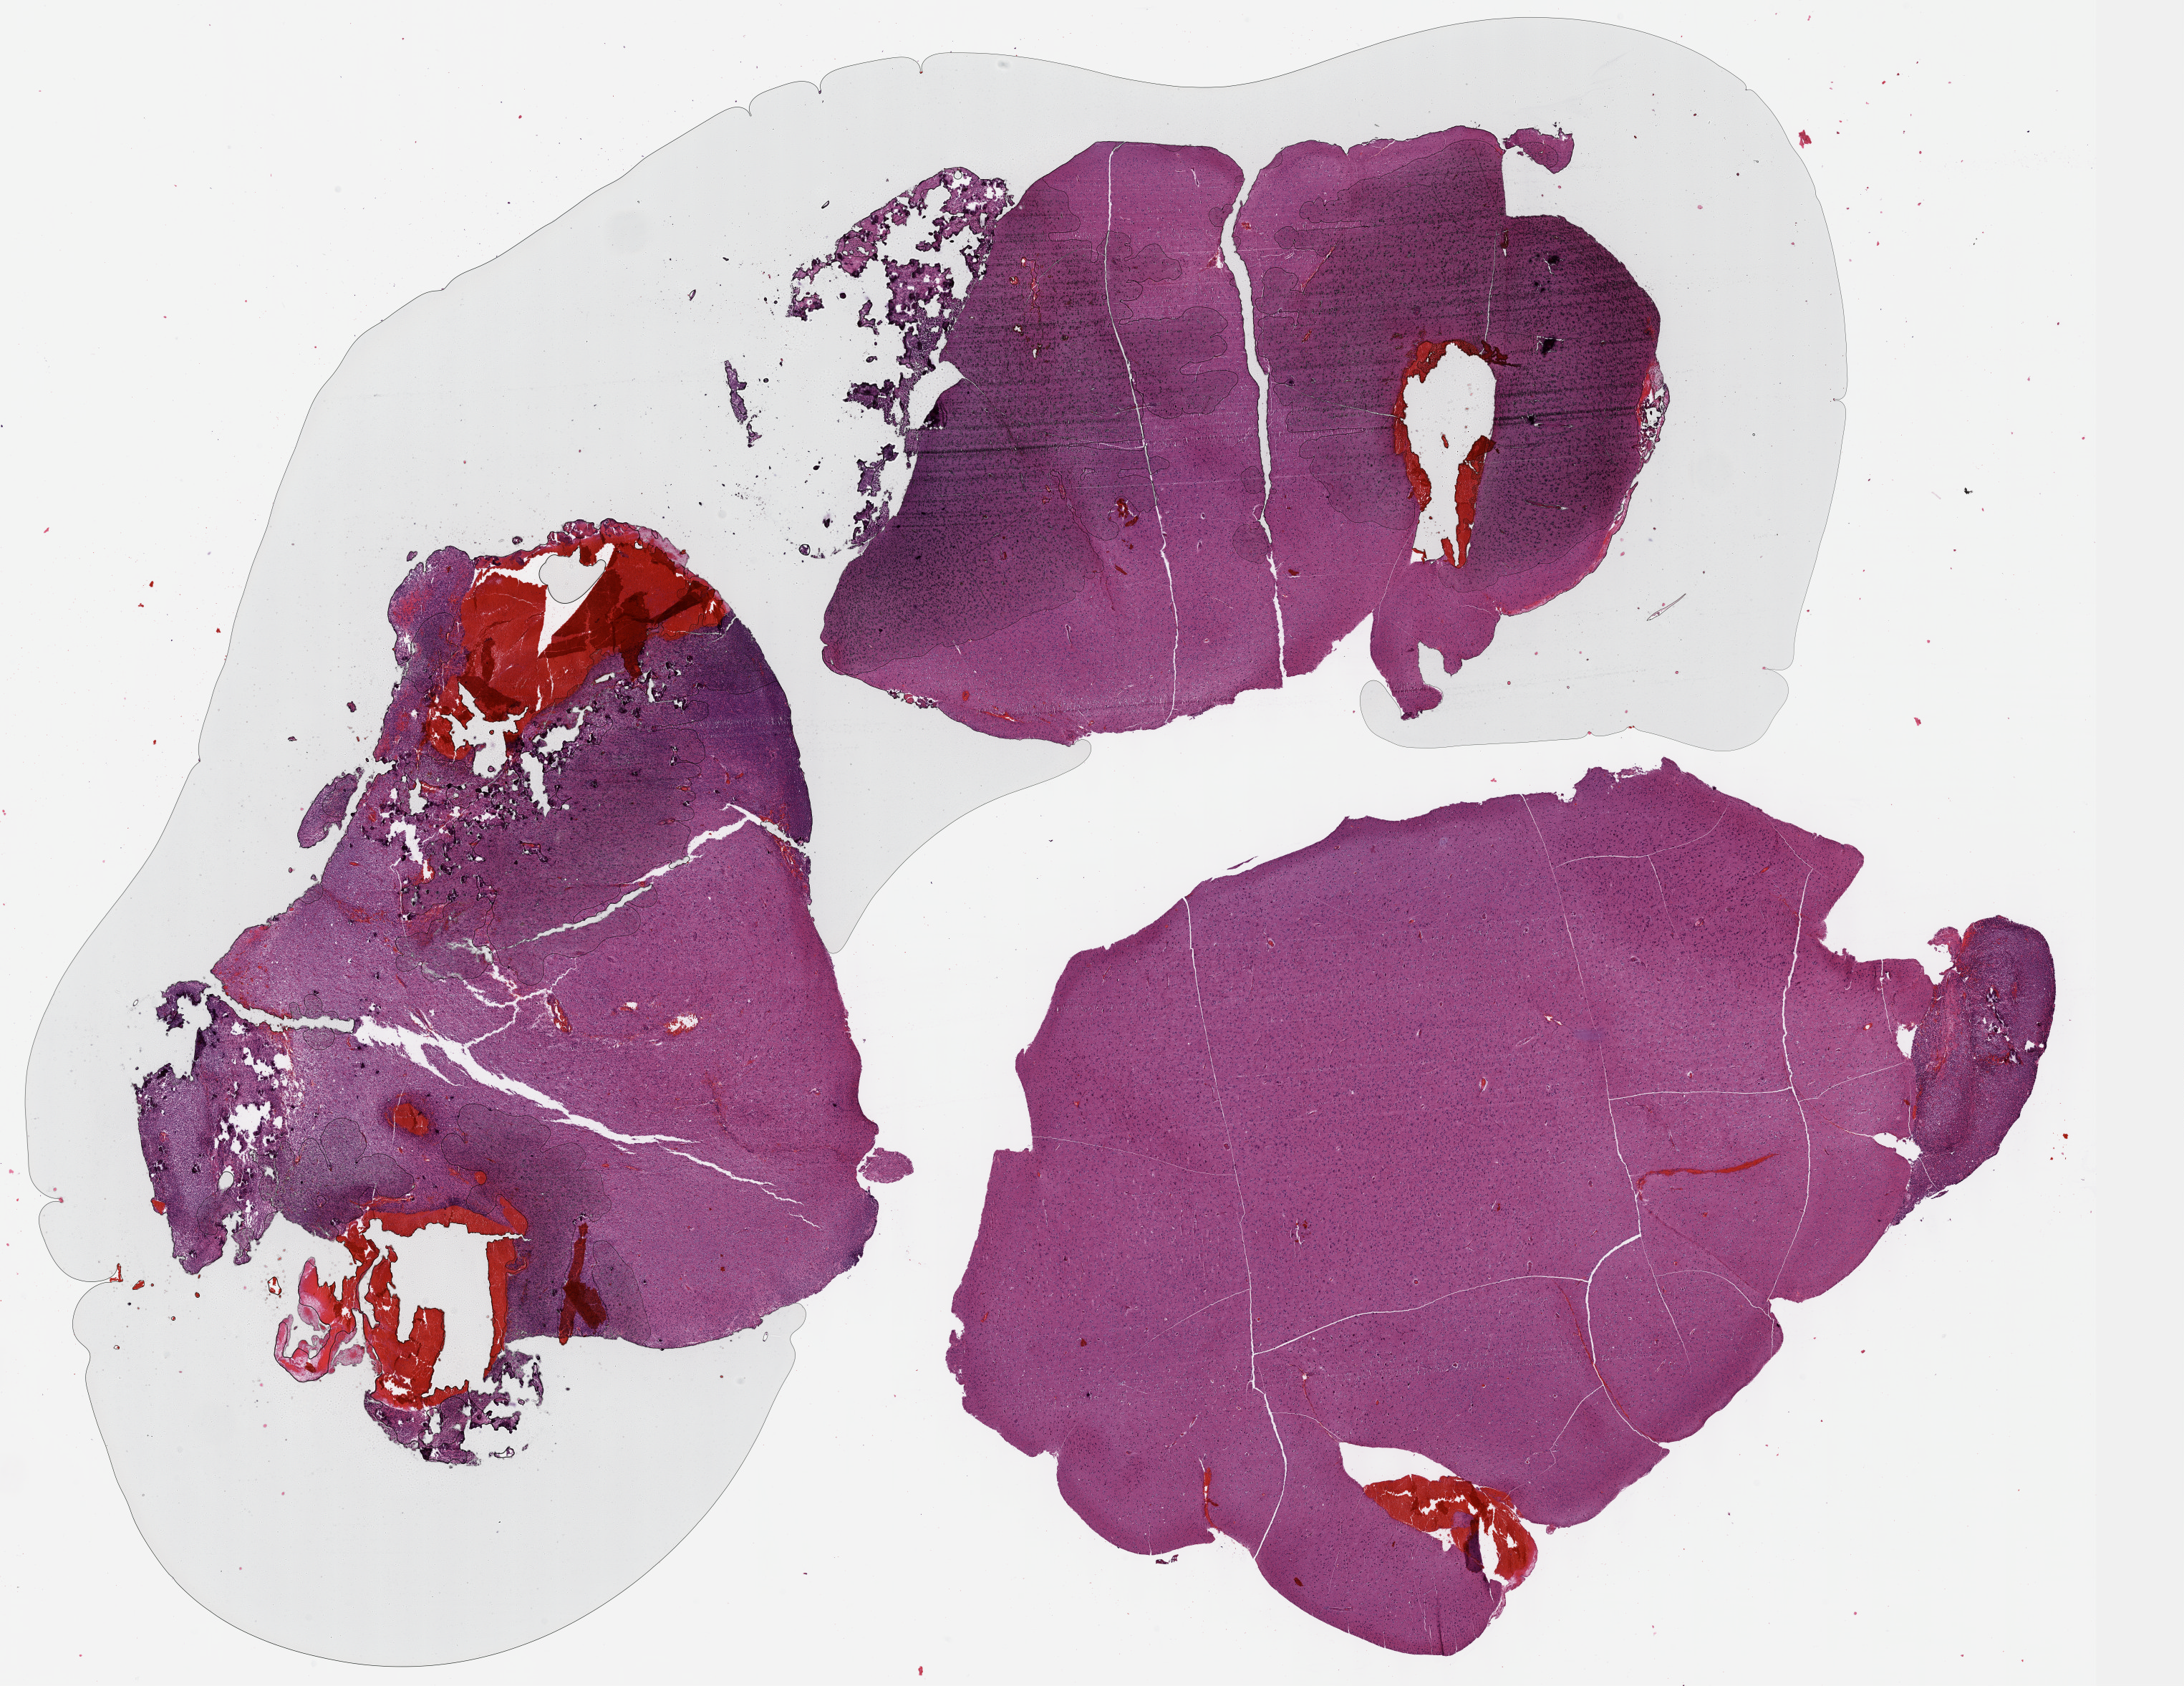
Digitized Hematoxylin and eosin (H&E) stained tissue section (whole slide), whole scanned area (about 24.6 x 19.0 mm, acquisition: 40x scan) shown as a low-resolution overview, formalin-fixed paraffin-embedded (FFPE) diagnostic section, sample: primary tumour, brain. Male, age 74 years at initial diagnosis. Histologic grade: G3 (poorly differentiated).
• laterality: right
• histologic diagnosis: Oligodendroglioma, anaplastic (cerebrum)